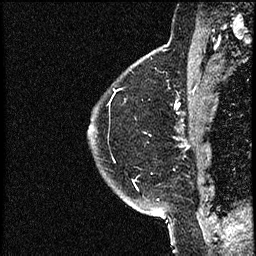
Breast MRI (dynamic contrast-enhanced), one sagittal slice; position 44 of 52 along the scan axis; dynamic contrast-enhanced study with each time point stored as its own series, time point 2 of 3 at this slice position (early post-contrast, ordered by acquisition time); 1.5 T; TE 4.2 ms, TR 17.6 ms; 256 × 256 image matrix. Female patient, age 49 years. From the clinical record (not read from this slice): setting: breast cancer imaged before/during neoadjuvant chemotherapy; receptor status: HER2-positive.
Structures marked on this image (semi-automatic segmentation, software-assisted and operator-edited):
- analysis volume of interest (the breast-tissue region the enhancement analysis was run in; not a lesion): bounding box [x1, y1, x2, y2] px = [89, 65, 182, 175]
- tumour enhancement mask (voxels above the 100 % enhancement threshold inside the analysis volume of interest): [177, 105, 180, 107]